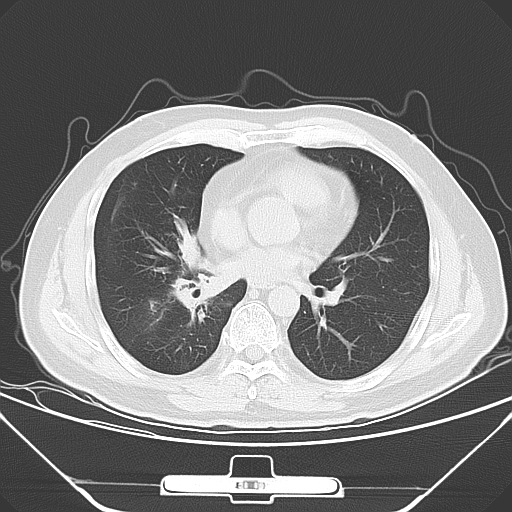
Chest CT, one axial slice. Slice 26 of 56 in the series (ordered by position). 120 kVp. Lung window (W 1500 / L -600 HU). 5 mm slice thickness. 512 × 512 image matrix, field of view 371 × 371 mm. Patient: male, 48 years. From the clinical record (not read from this slice): clinical TNM (as recorded): T1a N1 M1c.
Annotated regions visible in this slice (bounding box drawn by a radiologist):
- lung tumour (recorded histology: adenocarcinoma): bounding box [x1, y1, x2, y2] px = [168, 233, 223, 316]